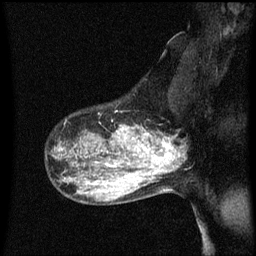
Breast MRI (dynamic contrast-enhanced), one sagittal slice. Slice 44 of 60 in the series (ordered by position). Dynamic contrast-enhanced series, image 2 of 3 at this slice position (ordered by acquisition). 1.5 T. TE 4.2 ms, TR 8.4 ms. 2 mm slice thickness. 256 × 256 image matrix. Patient: female, 50 years.
Structures marked on this image (semi-automatically segmented with operator editing):
- analysis volume of interest (the breast-tissue region the enhancement analysis was run in; not a lesion): bounding box <100,114,153,171> (left, top, right, bottom; pixels)
- tumour enhancement mask (voxels above the 70 % enhancement threshold inside the analysis volume of interest): <117,126,153,169>